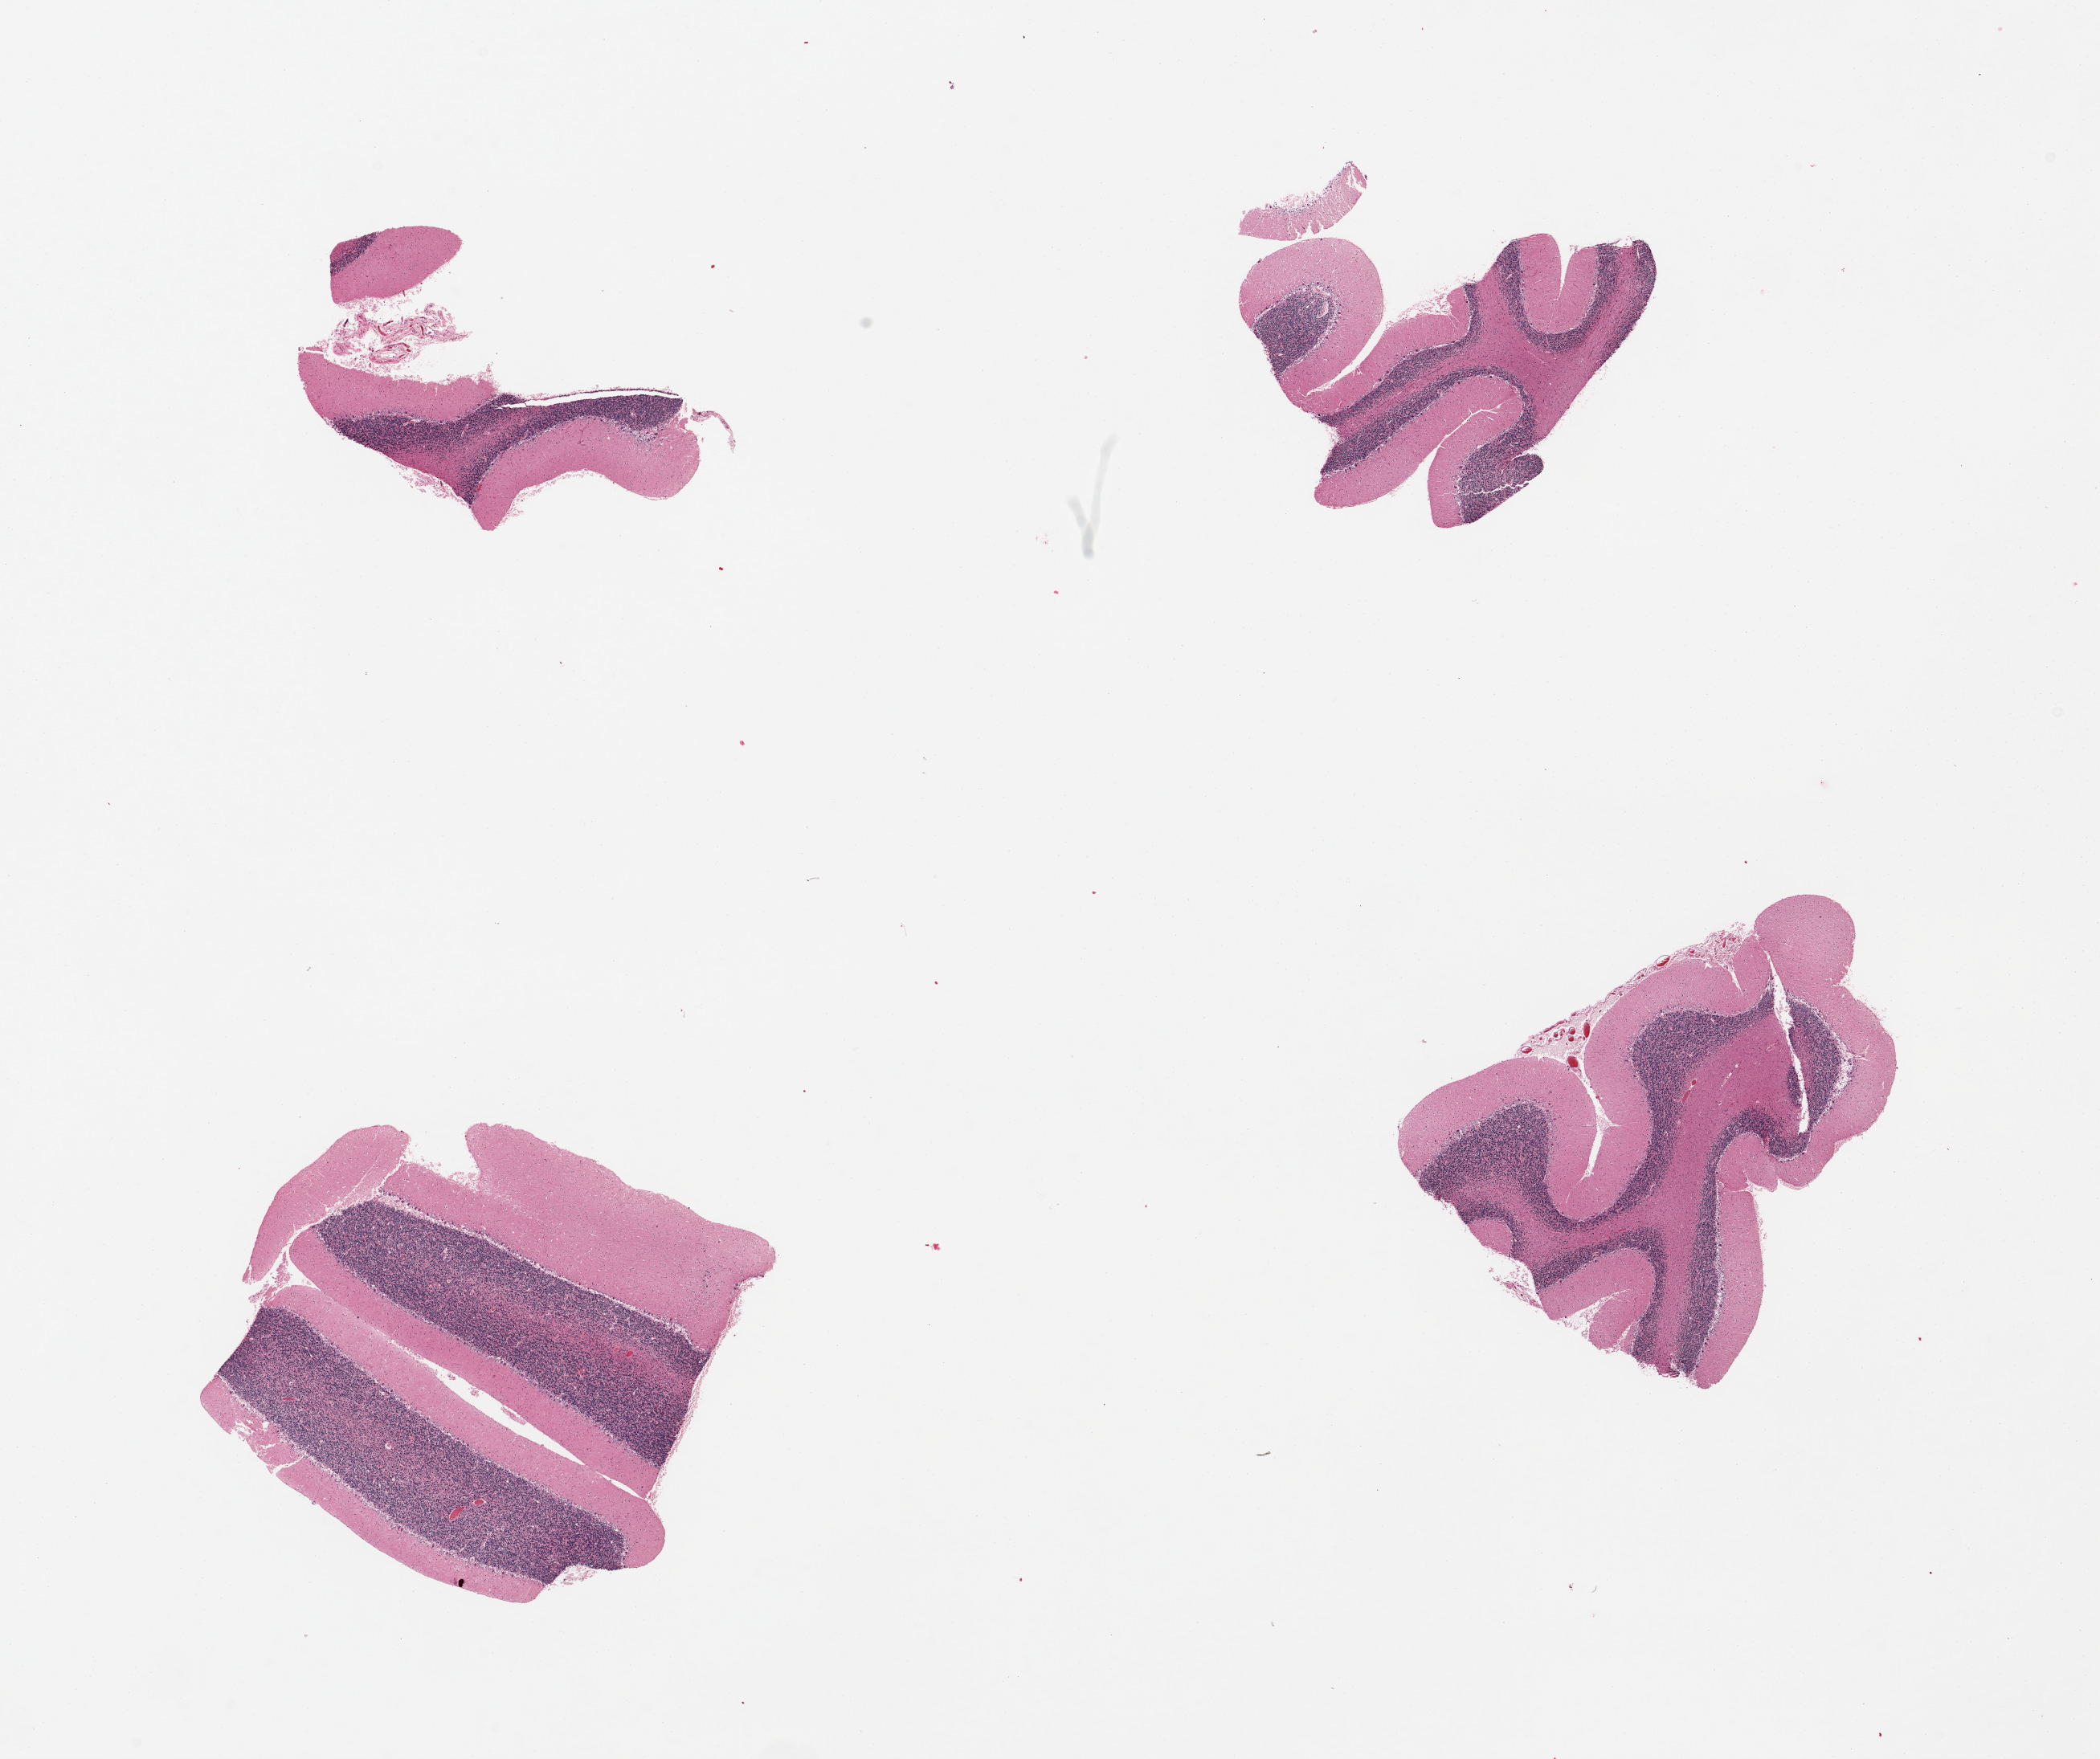
H&E whole-slide image, whole scanned area (about 20.7 x 17.3 mm) shown as a low-resolution overview. PAXgene-fixed, paraffin-embedded tissue. Sampled site (target tissue): cerebellum. Donor tissue sample. Donor sex: male.
Review note (as recorded): 4 pieces.